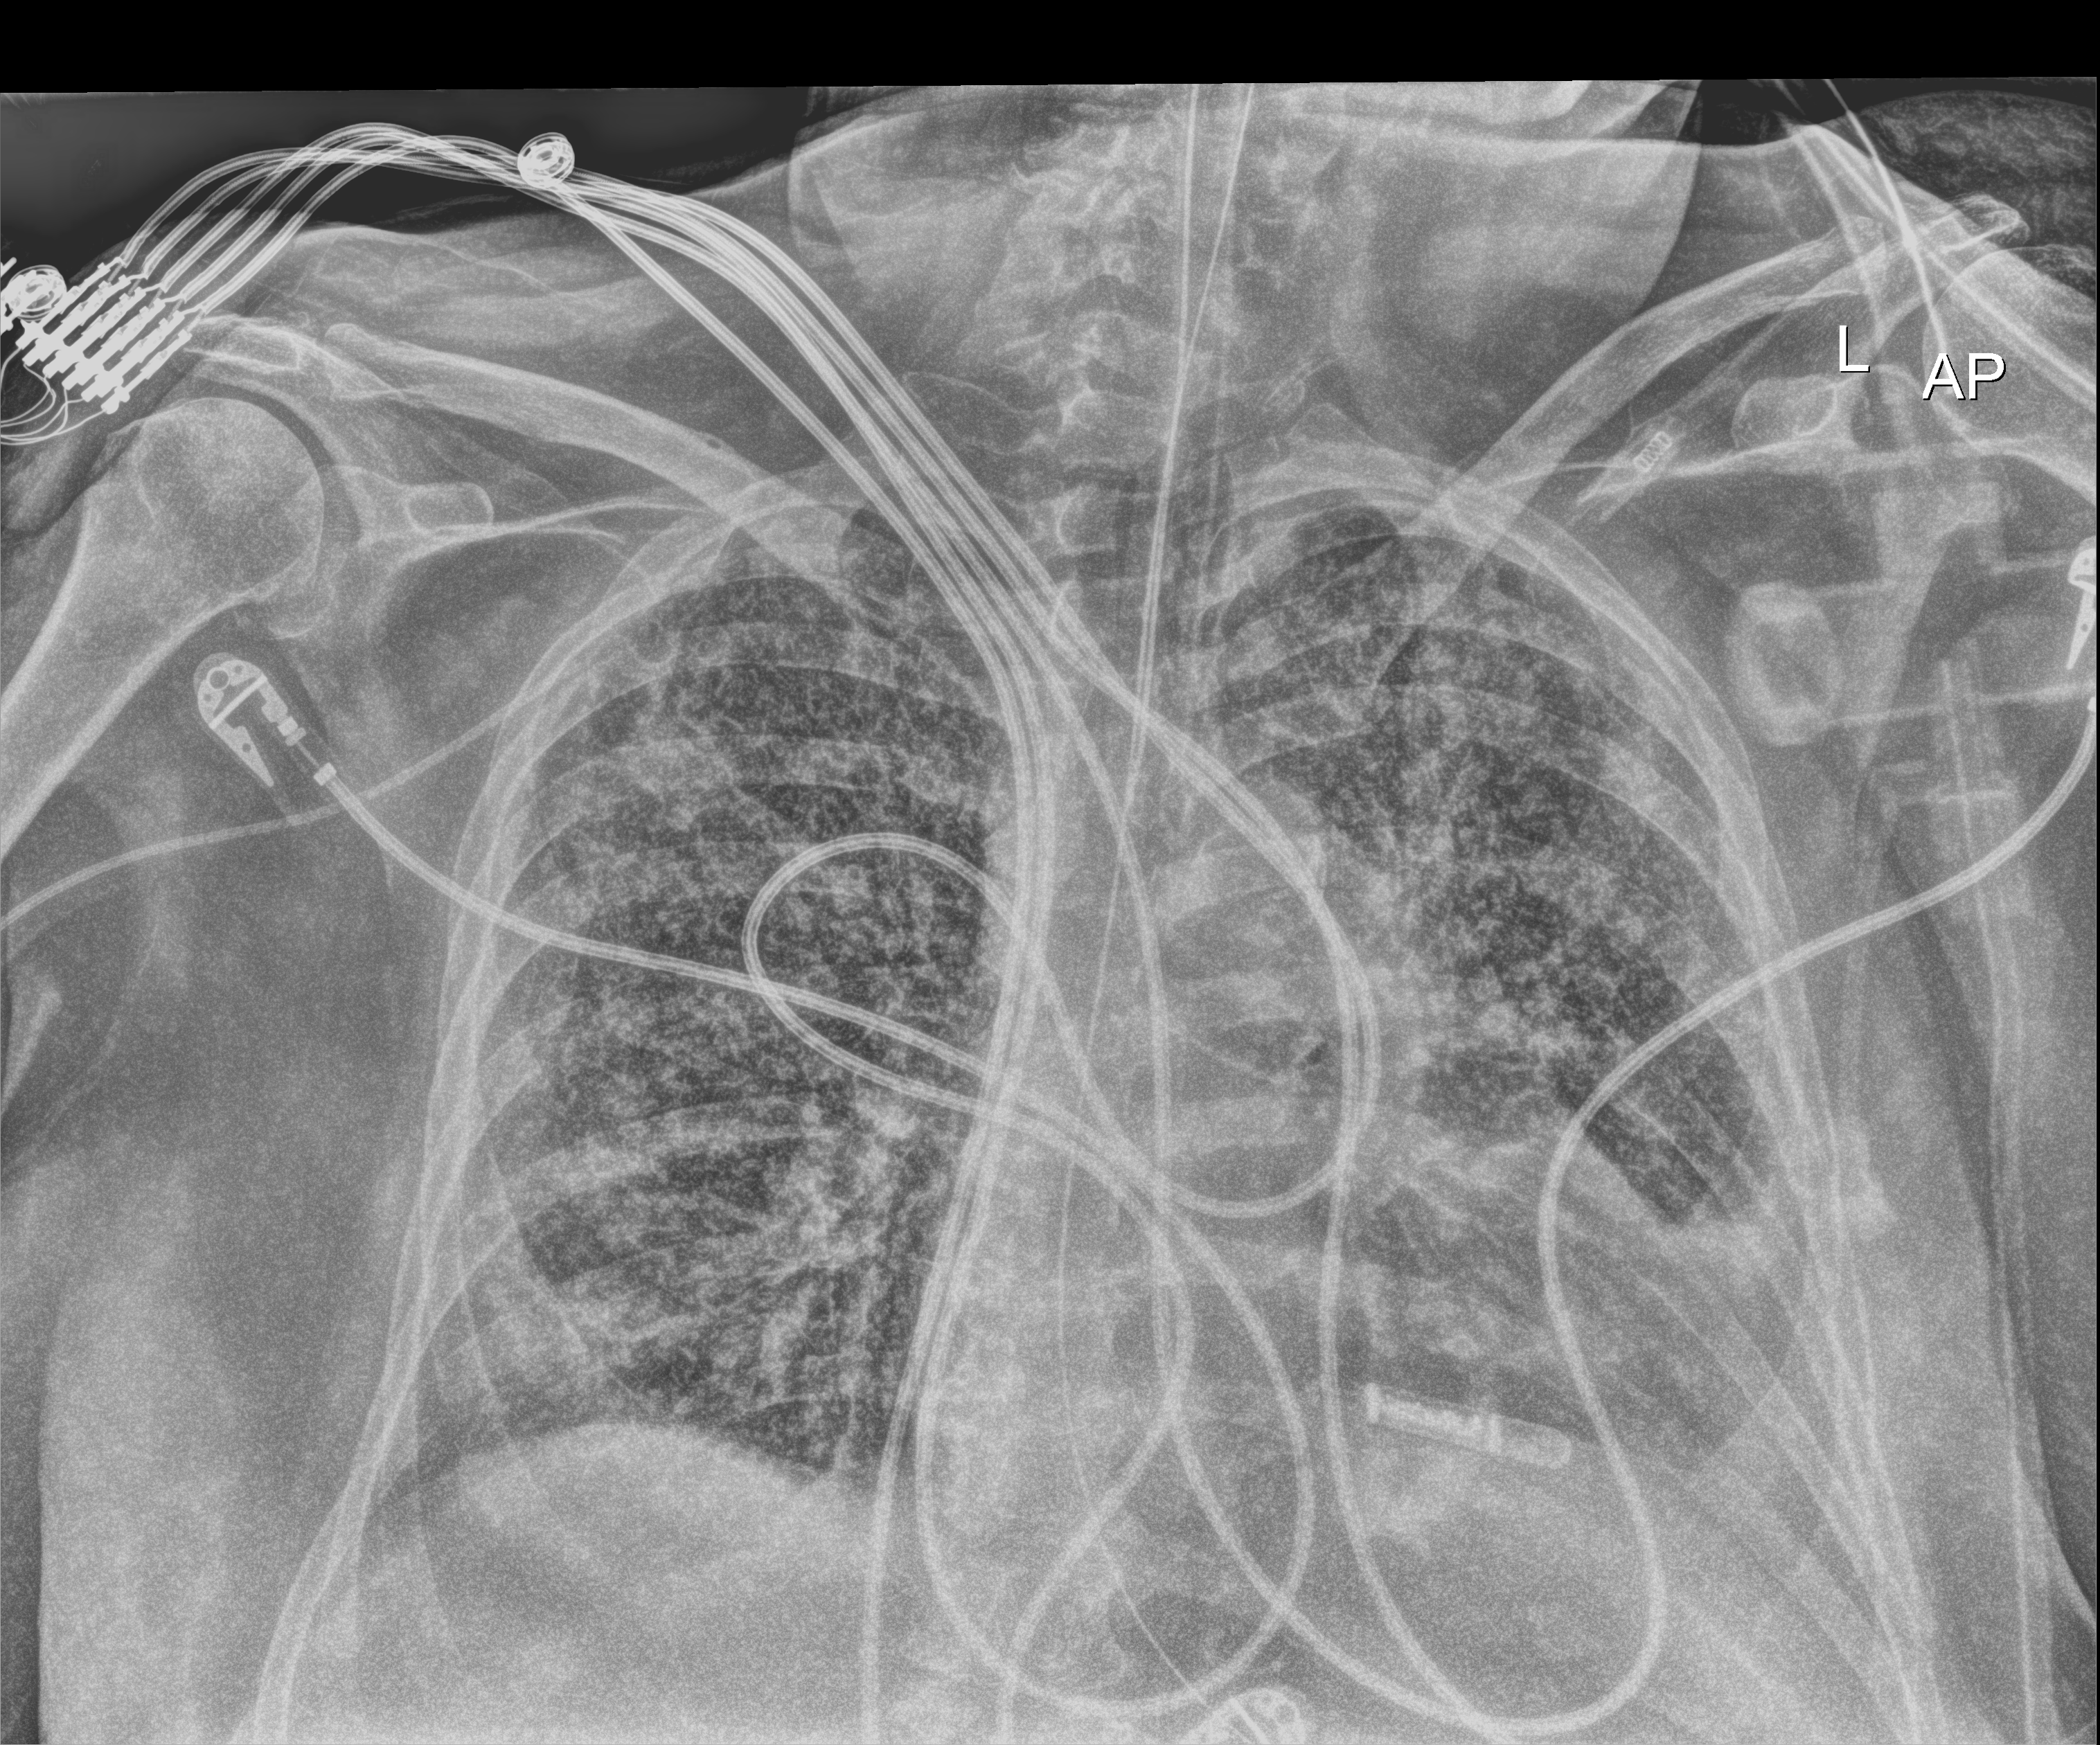
Chest X-ray (portable); anteroposterior (AP) projection. Female patient hospitalised with COVID-19, age 60–74 years.
From the hospital-stay record, not from the radiograph (when in the stay this image was taken is not recorded): admitted to intensive care during this hospital stay: yes; mechanically ventilated during this hospital stay: yes.